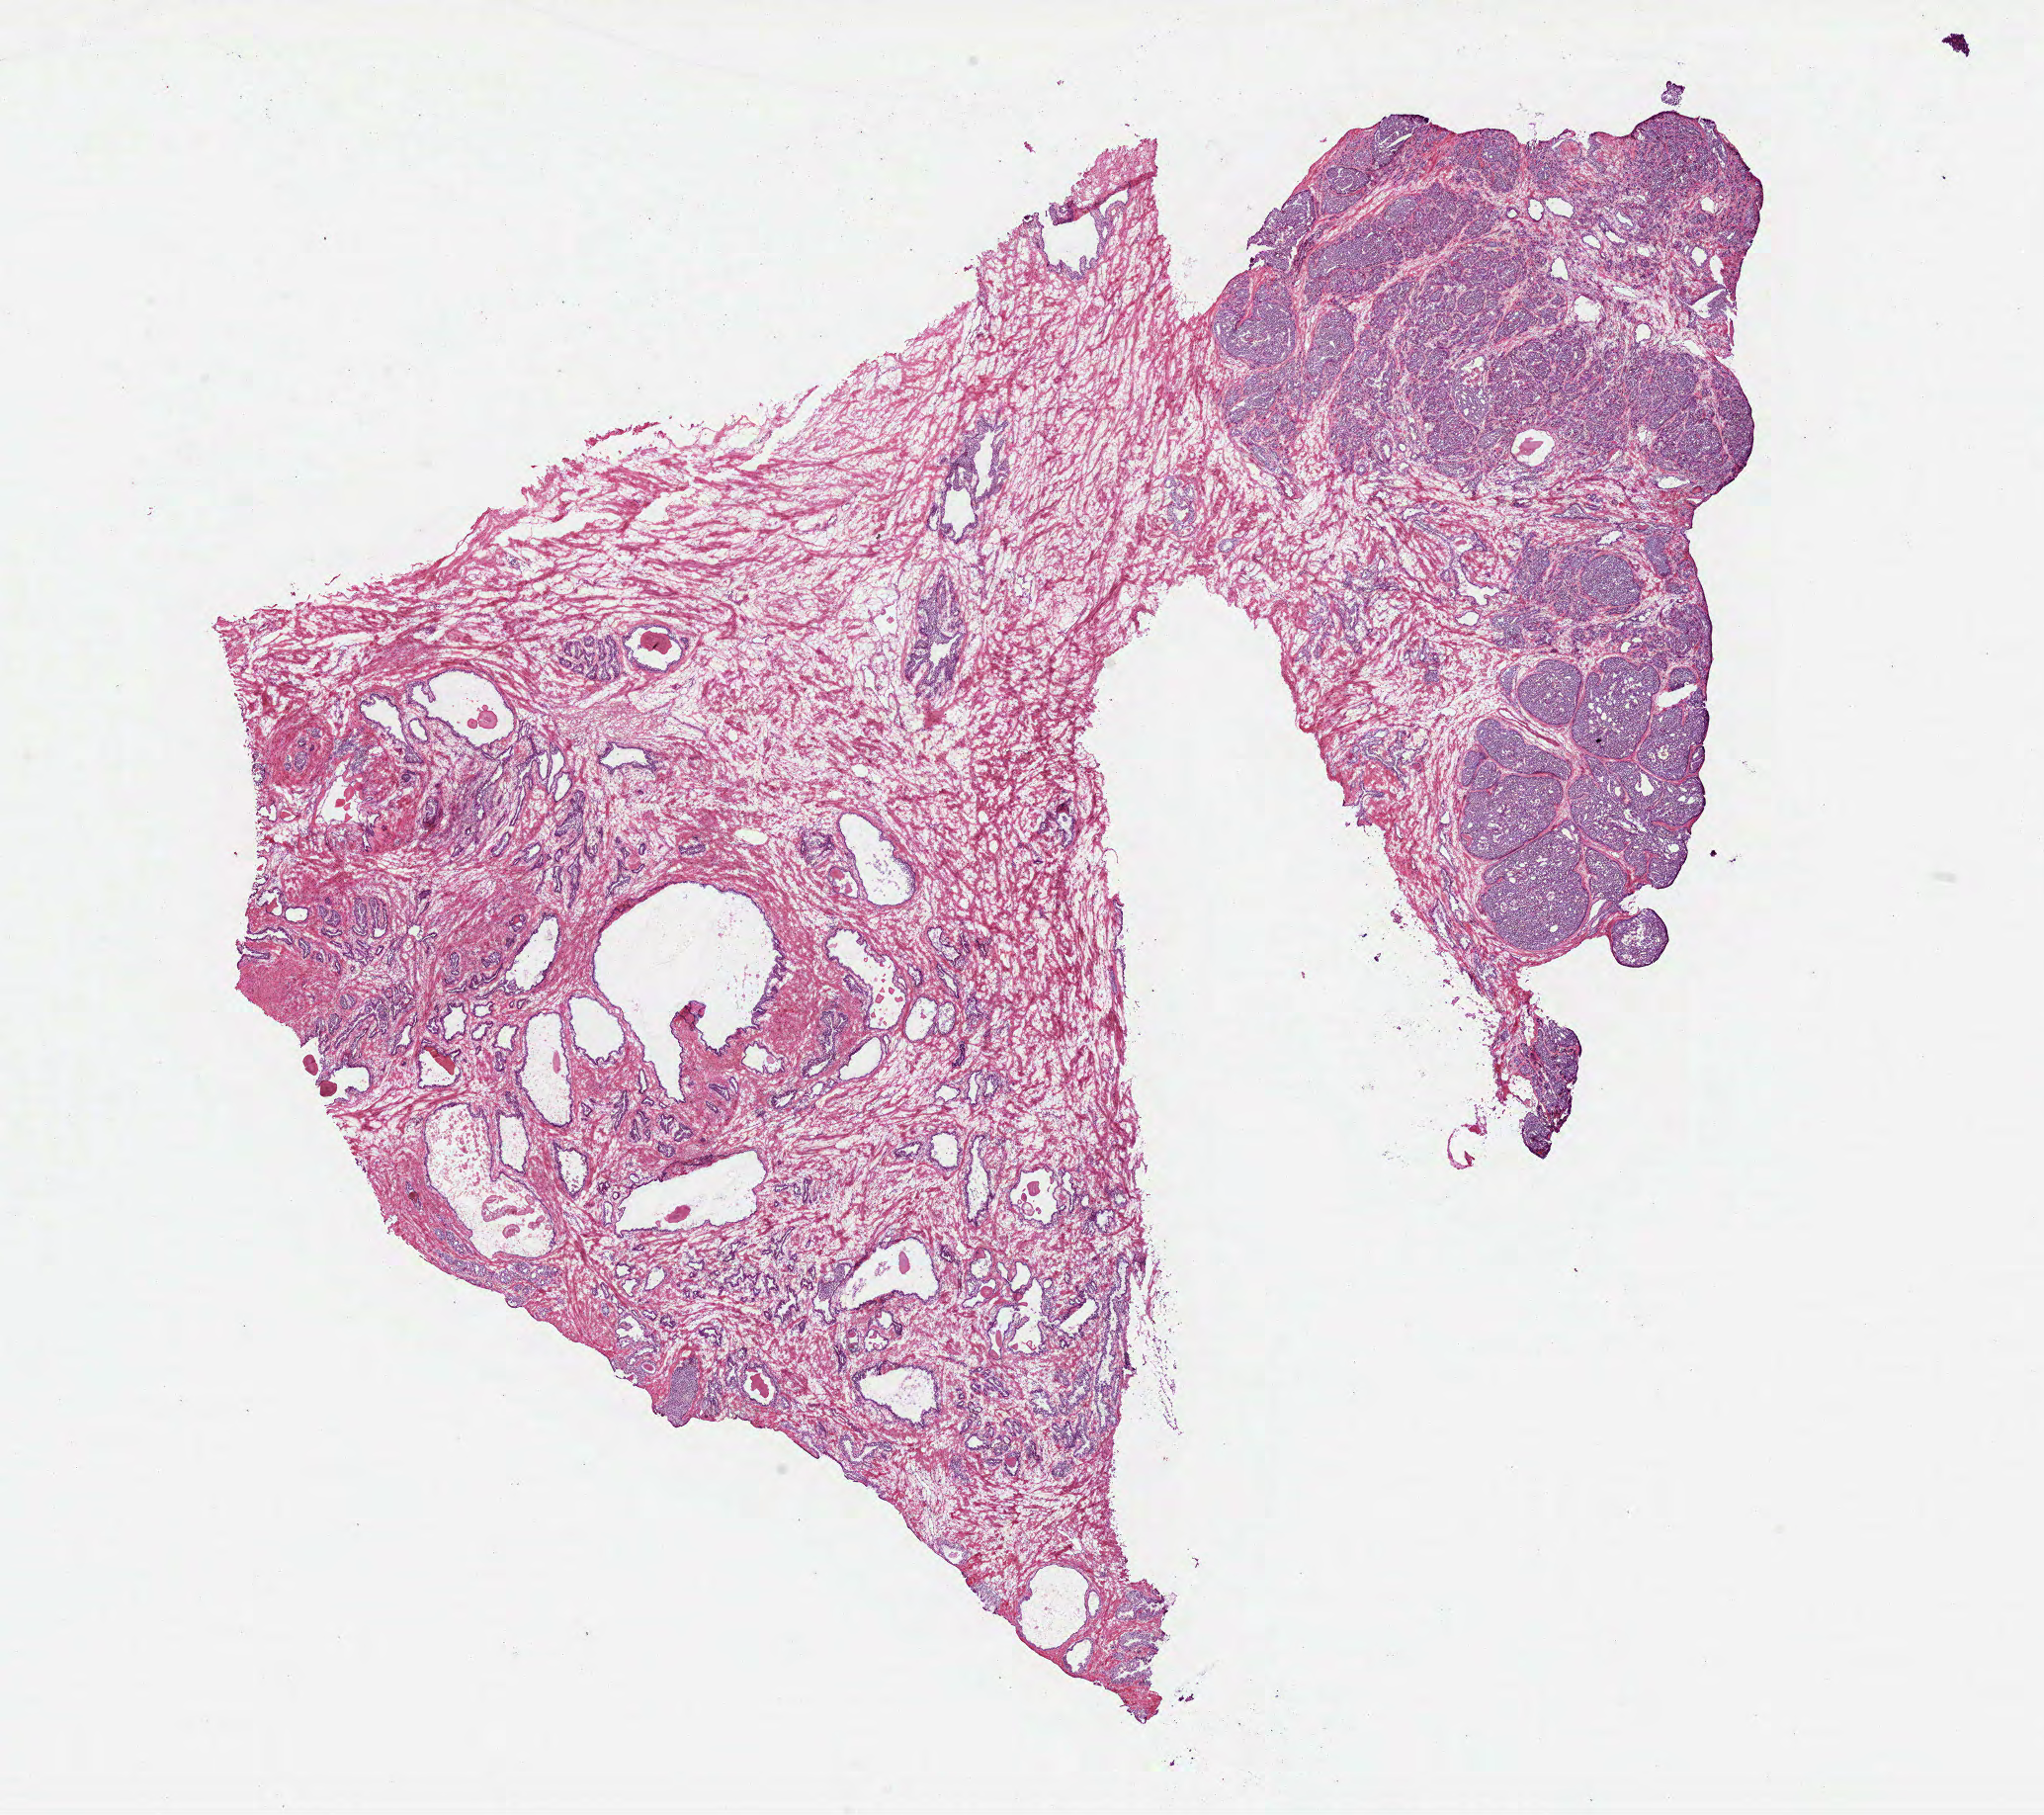
Whole-slide histology image, Hematoxylin and eosin (H&E) stained, a low-resolution overview of the entire scanned area, about 16.7 x 14.8 mm, frozen section from the bottom of the tissue portion, prostate, primary tumour sample. Patient: male, age at initial diagnosis 70 years. Gleason score: 7 (4+3). Pathologist review of this section (percent, as recorded): tumour cells 25%, tumour nuclei 25%, normal cells 50%, stromal cells 25%, necrosis 0%. Infiltration values recorded for this section: lymphocyte infiltration 0%, monocyte infiltration 0%, neutrophil infiltration 0%.
Pathologic diagnosis: Acinar cell carcinoma. Laterality: bilateral.